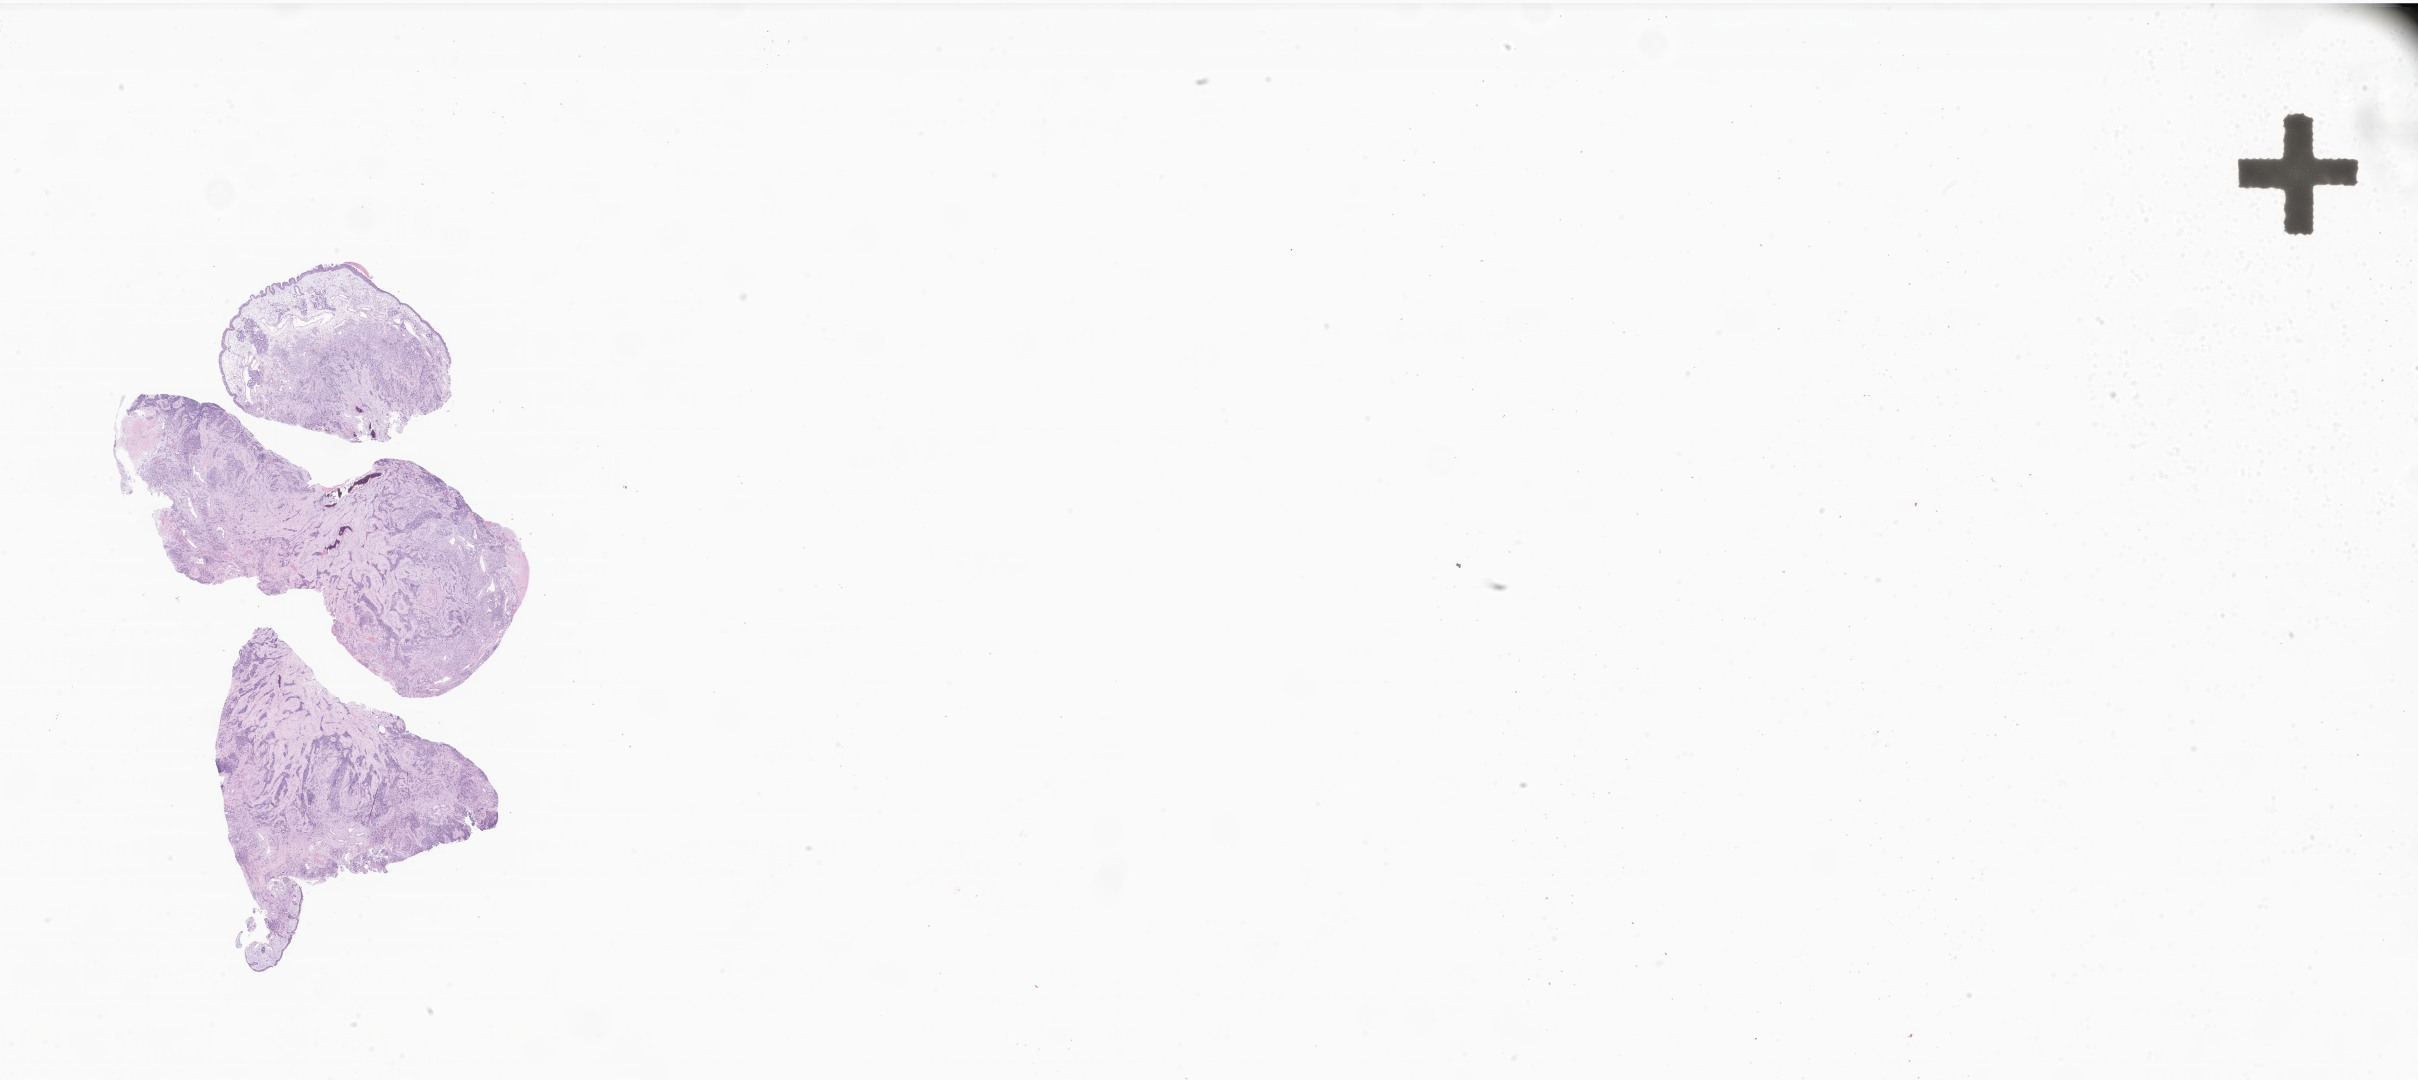
Whole-slide image, haematoxylin and eosin stain of tumor tissue from the nasal cavity — low-resolution overview of the scanned area, about 40.8 x 18.2 mm; formalin-fixed, paraffin-embedded (FFPE) tissue. Patient: female, age 94 months.
• diagnosis: Alveolar rhabdomyosarcoma